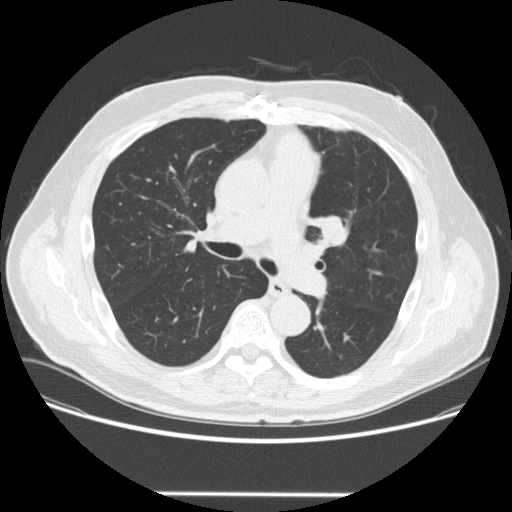
Low-dose screening chest CT, one axial slice. Slice 161 of 253 in the series (ordered by position). Reconstruction kernel STANDARD. Lung window (W 1500 / L -600 HU). 2.5 mm slice thickness. 512 × 512 image matrix, field of view 400 × 400 mm.
Structures marked on this image (outlined manually by an expert reader):
- lesion 1 (tumor, upper lobe of left lung): box from (x=319, y=217) to (x=344, y=244) px